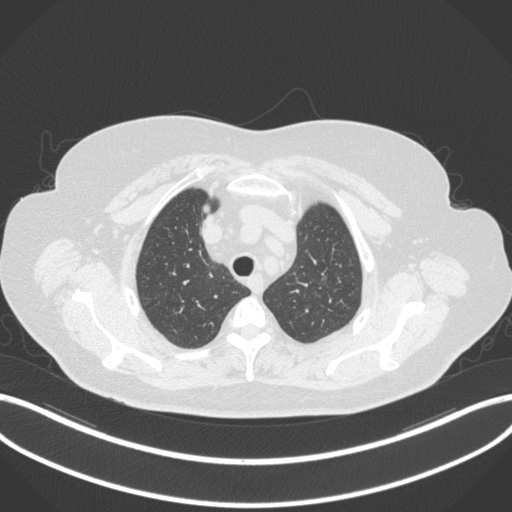
Chest CT, one axial slice. Slice 277 of 310 in the series (ordered by position). 120 kVp. Lung window (W 1500 / L -600 HU). 1 mm slice thickness. 512 × 512 image matrix, field of view 400 × 400 mm. Patient: female, 70 years. From the clinical record (not read from this slice): clinical TNM (as recorded): T1c N0 M0.
Outlined on this slice (rectangle marked by the reading radiologist):
- lung tumour (recorded histology: adenocarcinoma): bounding box <318,262,333,286> (left, top, right, bottom; pixels)